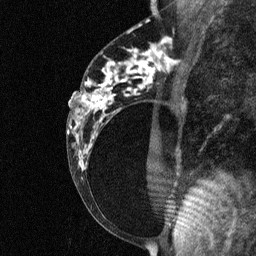
Breast MRI (dynamic contrast-enhanced), one sagittal slice; slice 32 of 64 in the series (ordered by position); dynamic contrast-enhanced study with each time point stored as its own series, time point 2 of 3 at this slice position (early post-contrast, ordered by acquisition time); 1.5 T; TE 4.8 ms, TR 27 ms; 2 mm slice thickness; 256 × 256 image matrix, field of view 180 × 180 mm. Female patient, age 34 years. Case-level facts recorded for this patient, not image findings: setting: breast cancer imaged before/during neoadjuvant chemotherapy; receptor status: HR-positive, HER2-negative.
Structures marked on this image (semi-automatic segmentation, software-assisted and operator-edited):
- analysis volume of interest (the breast-tissue region the enhancement analysis was run in; not a lesion): bounding box (x1, y1, x2, y2) in pixels: (78, 44, 181, 191)
- tumour enhancement mask (voxels above the 90 % enhancement threshold inside the analysis volume of interest): (81, 50, 163, 168)